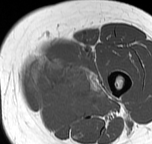
MRI of an extremity soft-tissue mass, one axial slice. Position 17 of 57 along the scan axis. MR volume resampled by the dataset authors to the PET/CT grid (not the native acquisition matrix). 3.27 mm slice thickness. 152 × 144 image matrix, field of view 148 × 141 mm. Female patient. Case-level facts recorded for this patient, not image findings: histological type: pleiomorphic leiomyosarcoma; grade: intermediate; site of the primary tumour: left thigh.
Annotated regions visible in this slice (expert contour drawn on MRI and transferred to this co-registered scan by the dataset authors):
- gross tumour volume including surrounding oedema: bounding box [x1, y1, x2, y2] px = [27, 53, 105, 100]
- gross tumour volume (mass): [29, 55, 90, 100]